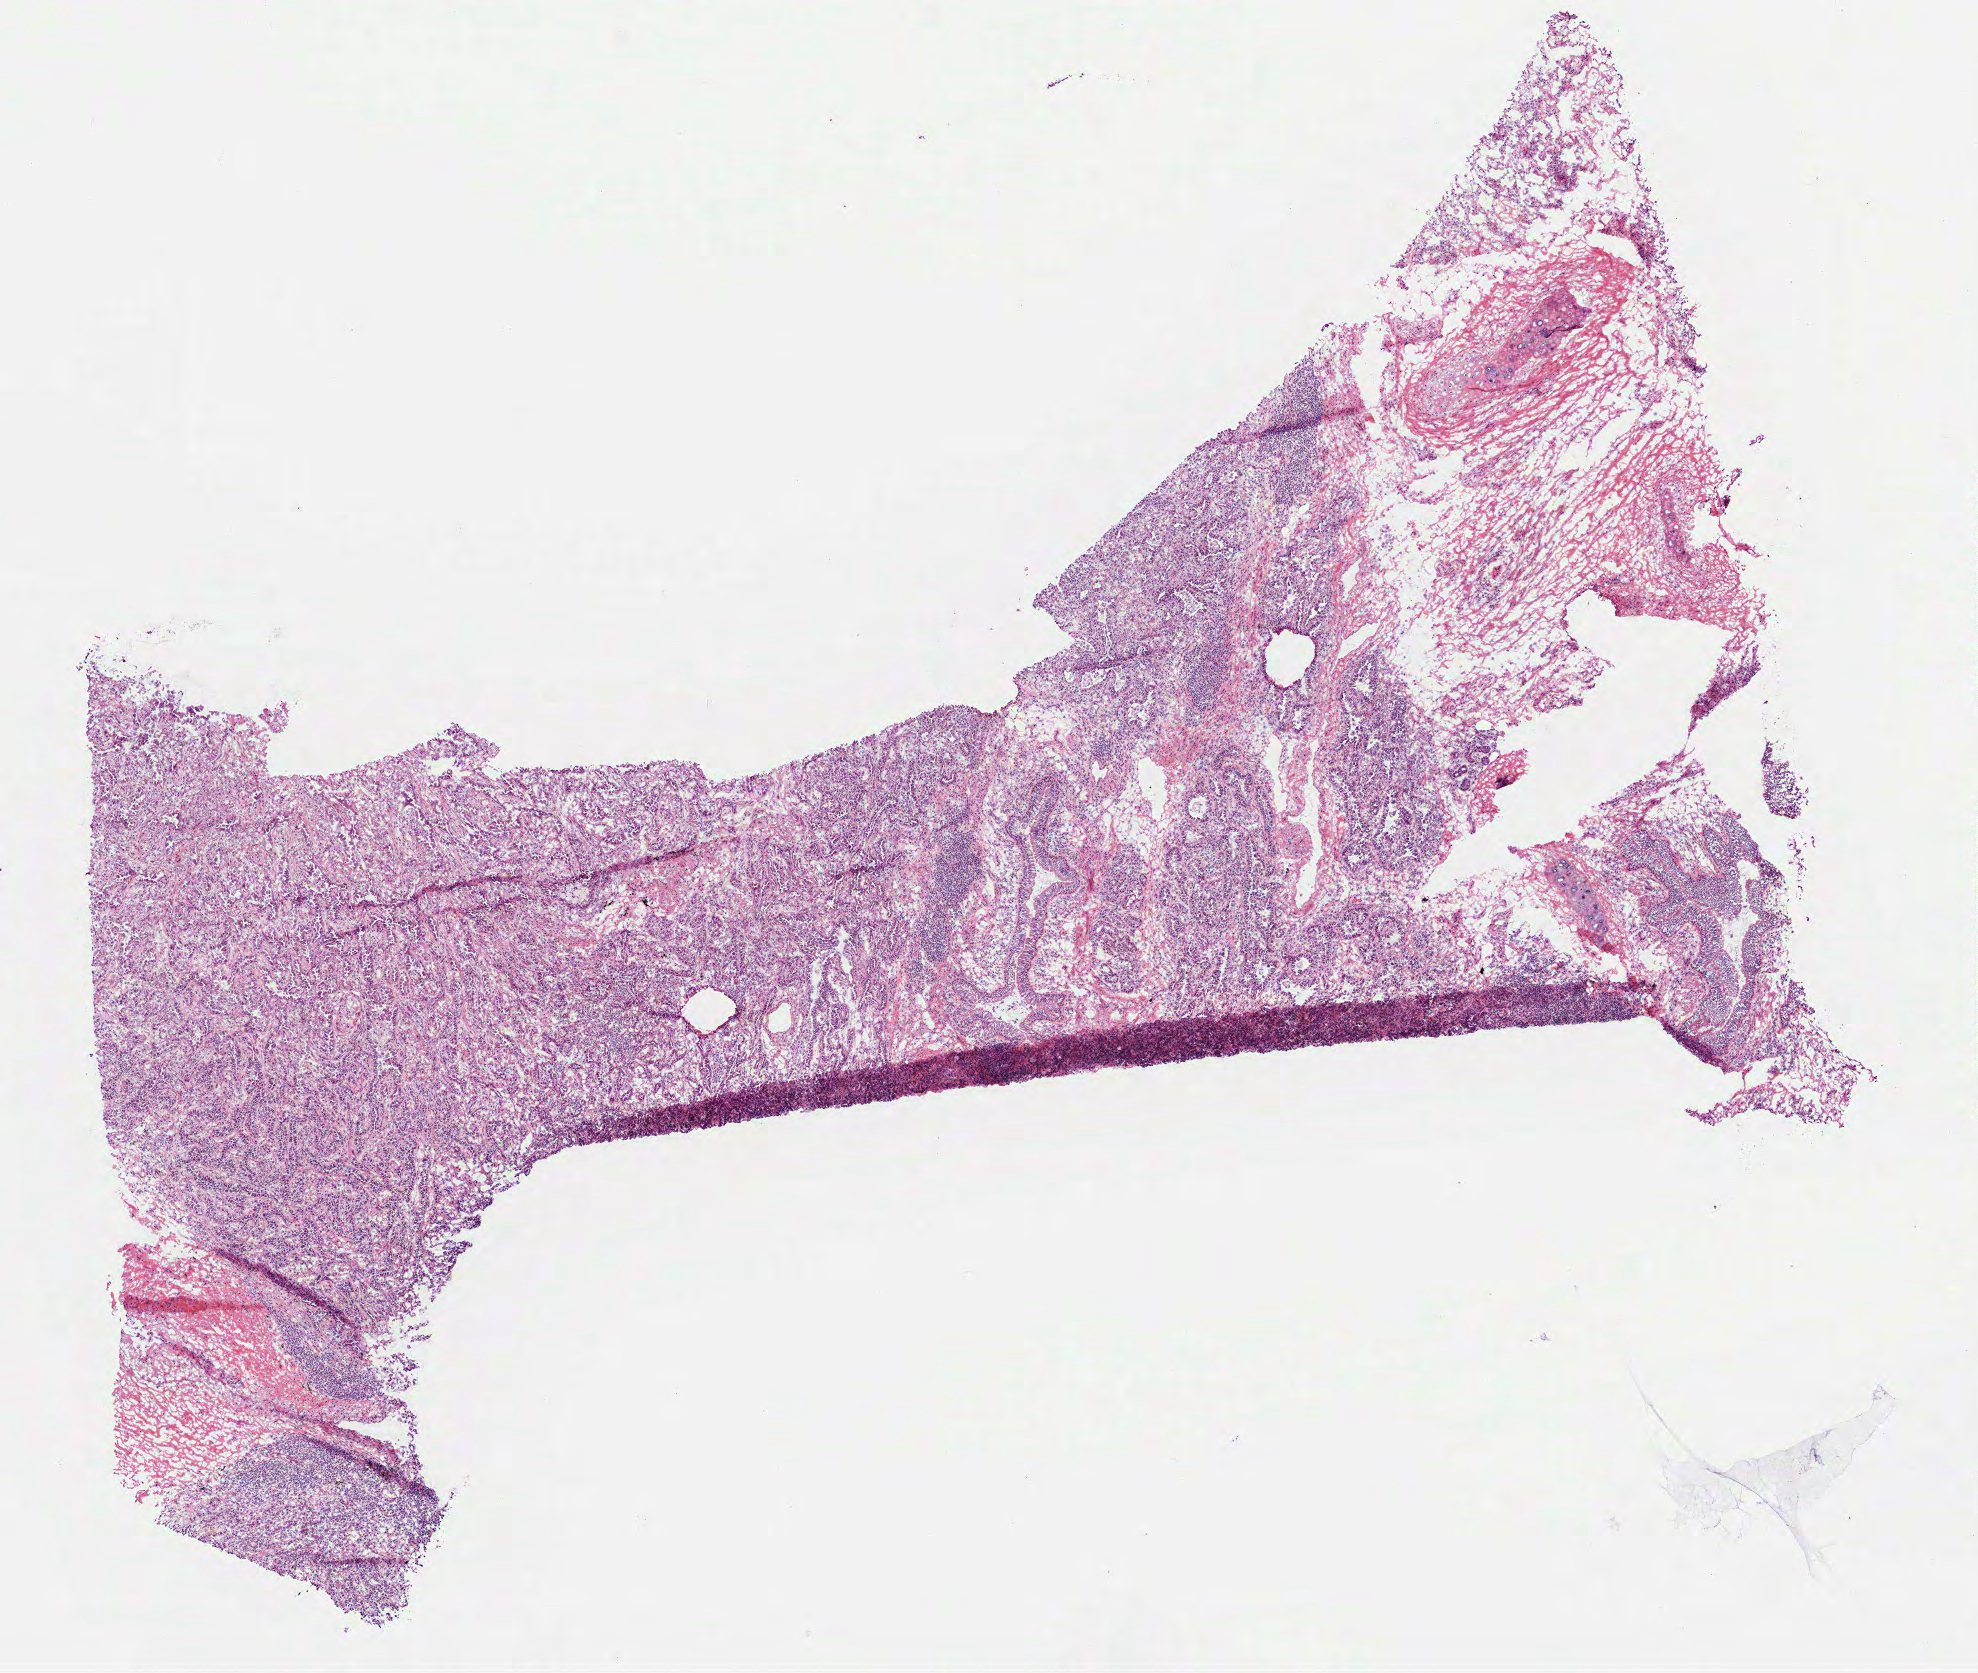
Whole-slide histology image, H&E-stained, whole scanned area (about 8.0 x 6.7 mm) shown as a low-resolution overview, frozen section from the bottom of the tissue portion, sample: primary tumour, lung. Female patient; age at initial diagnosis 72 years. Pathologist review of this section (percent, as recorded): tumour cells 80%, tumour nuclei 65%, normal cells 5%, stromal cells 15%, necrosis 0%.
- AJCC pathologic stage: IA (7th edition)
- diagnosis: Adenocarcinoma, NOS